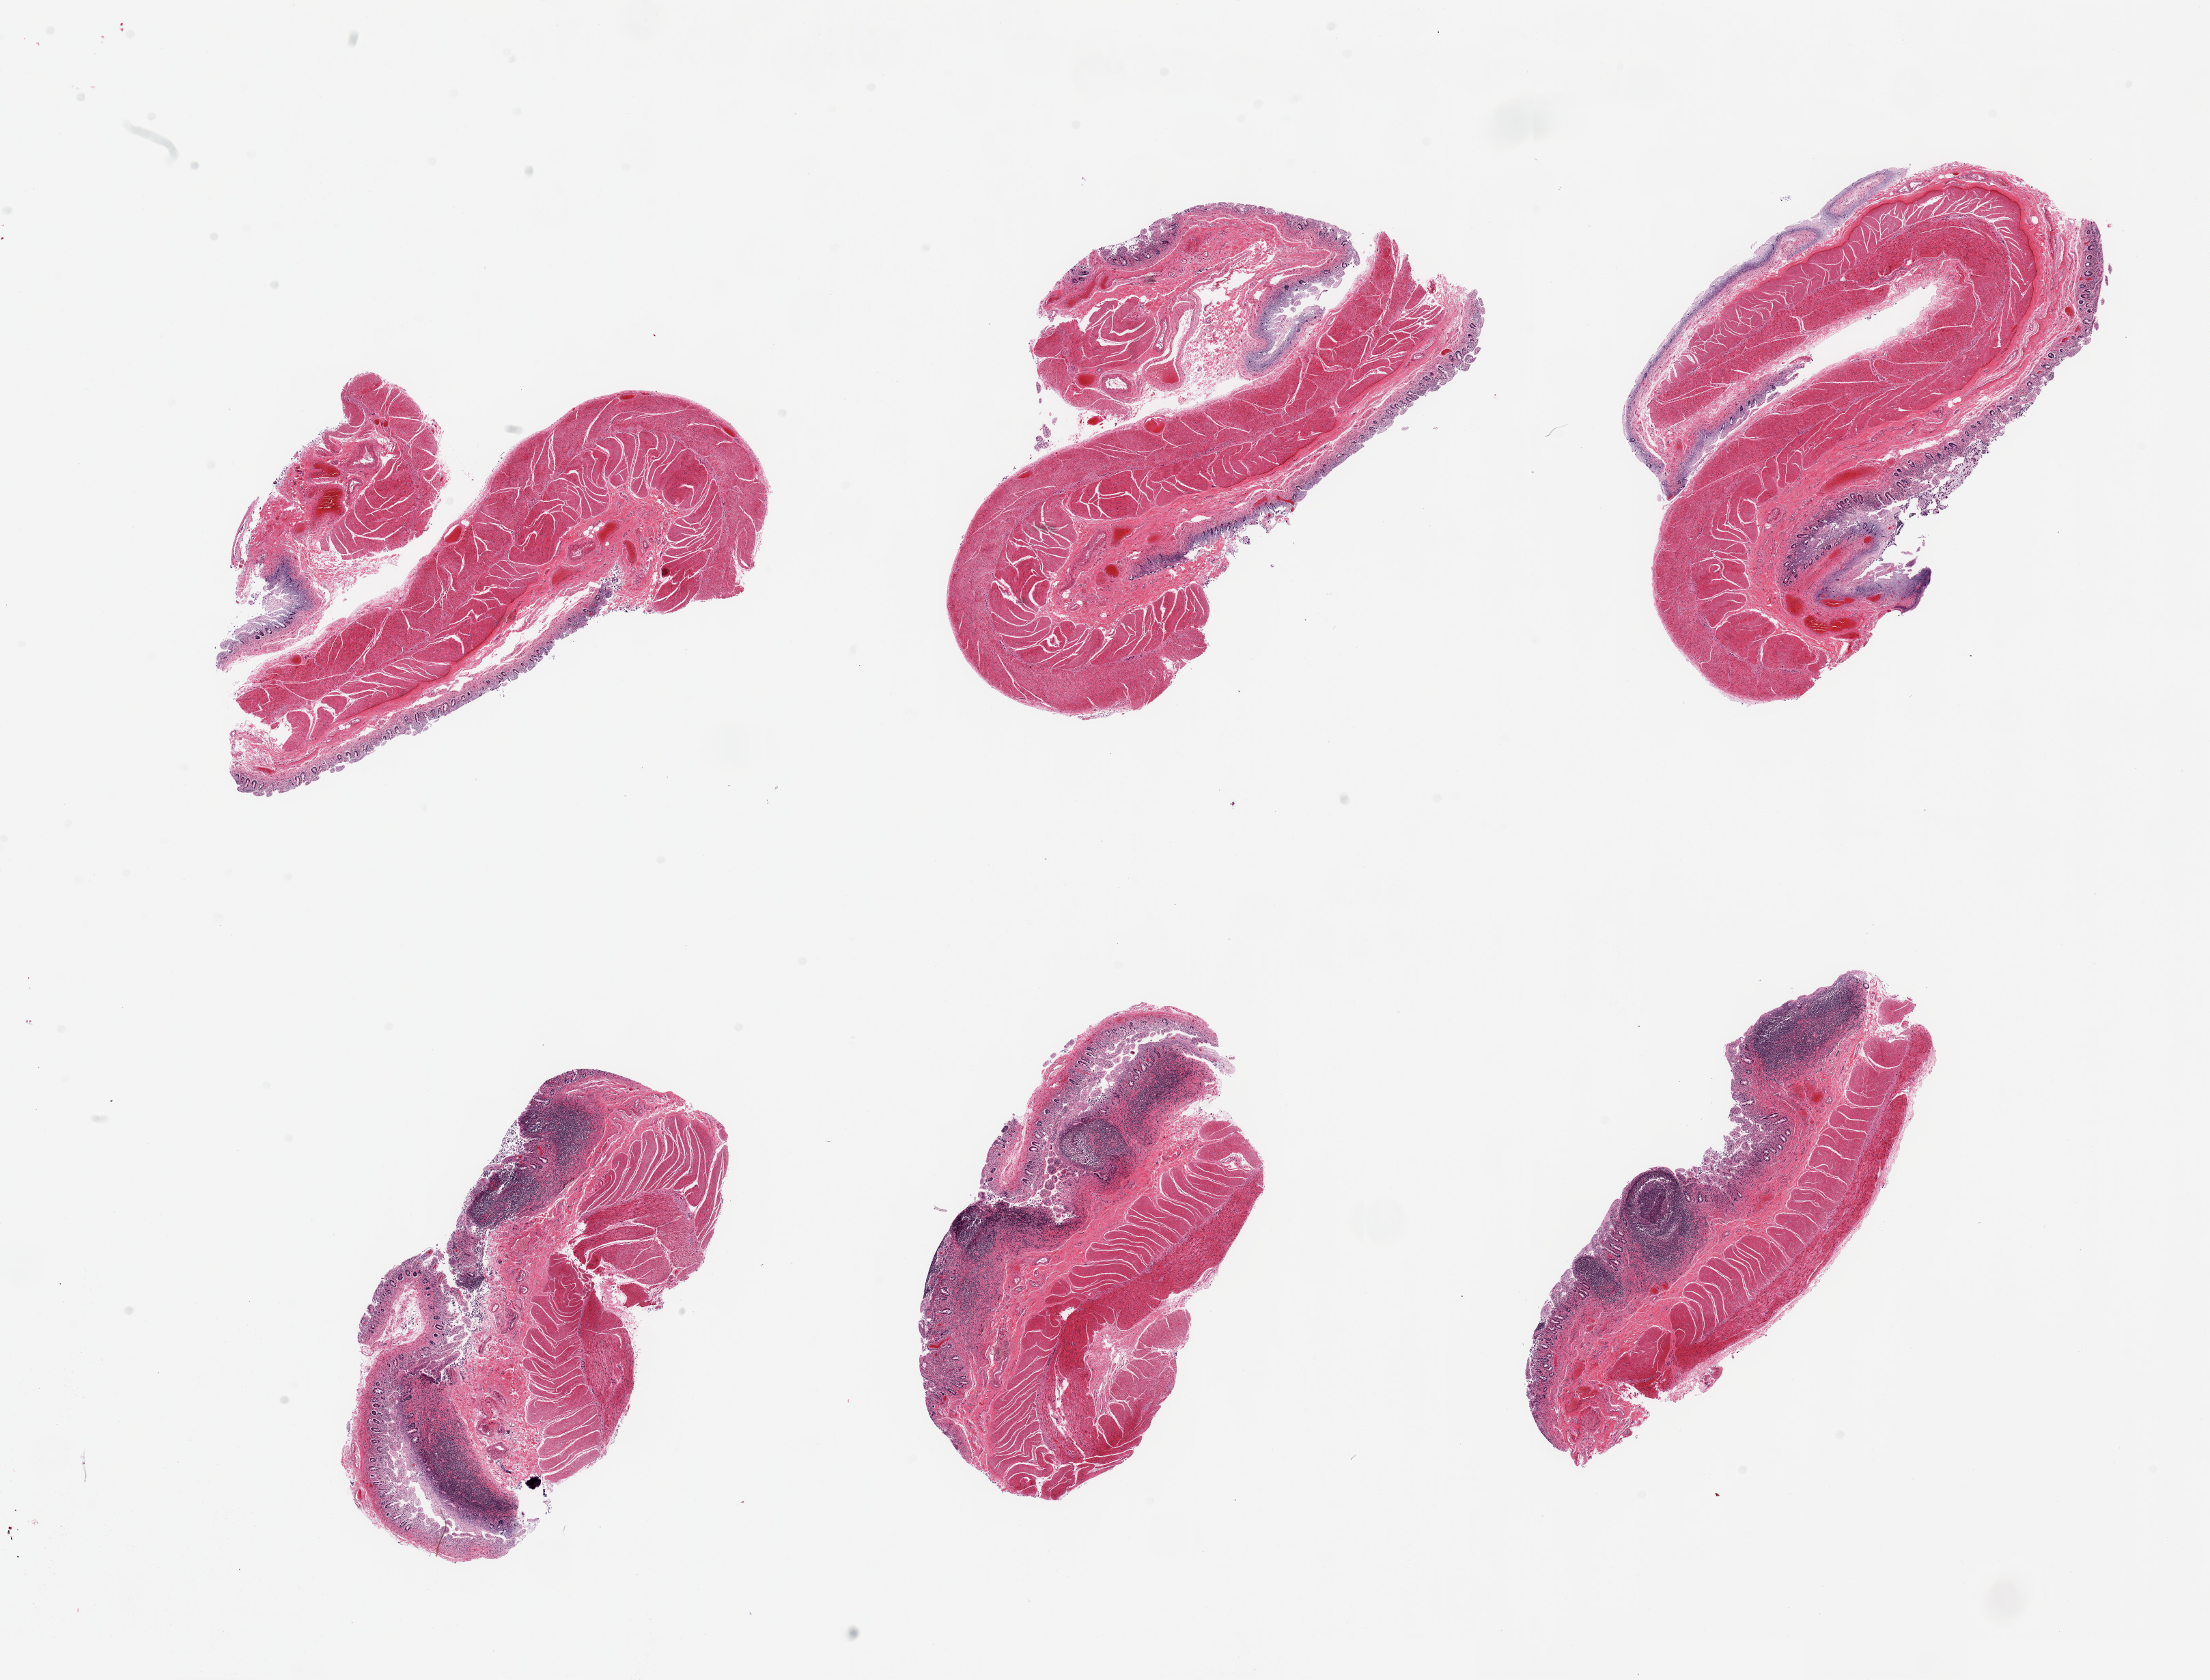
Digitized H&E-stained section, low-resolution overview of the scanned area, about 25.6 x 19.5 mm. PAXgene-fixed, paraffin-embedded tissue. Sampled site (target tissue): ileum. Tissue donor sample. Female donor.
Reviewer comment on this tissue sample: 6 pieces; full thickness sections (muscularis is not target), only scattered lymphoid follicles.